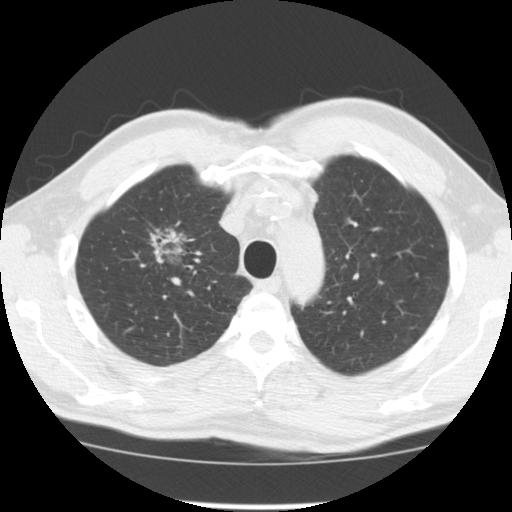
Low-dose screening chest CT, axial slice, third screening round (two years after baseline), lung window (W 1500 / L -600 HU), 2.5 mm slice thickness, standard (soft-tissue) reconstruction kernel (STANDARD), slice 30 of 128 in the series. Male, age 64 years at enrolment.
Expert reader's lesion annotation, bounding box <129,217,208,282> (left, top, right, bottom; pixels). The screening reader recorded 3 non-calcified nodules or masses ≥4 mm on this exam (right upper lobe, right lower lobe, left upper lobe); which of them this box marks is not recorded. Official screen result: positive, other. Later outcome: lung cancer diagnosed 30 days after this screen — adenocarcinoma, NOS, right upper lobe, well differentiated (G1), stage IB (AJCC 6th edition), 45 mm at pathology.